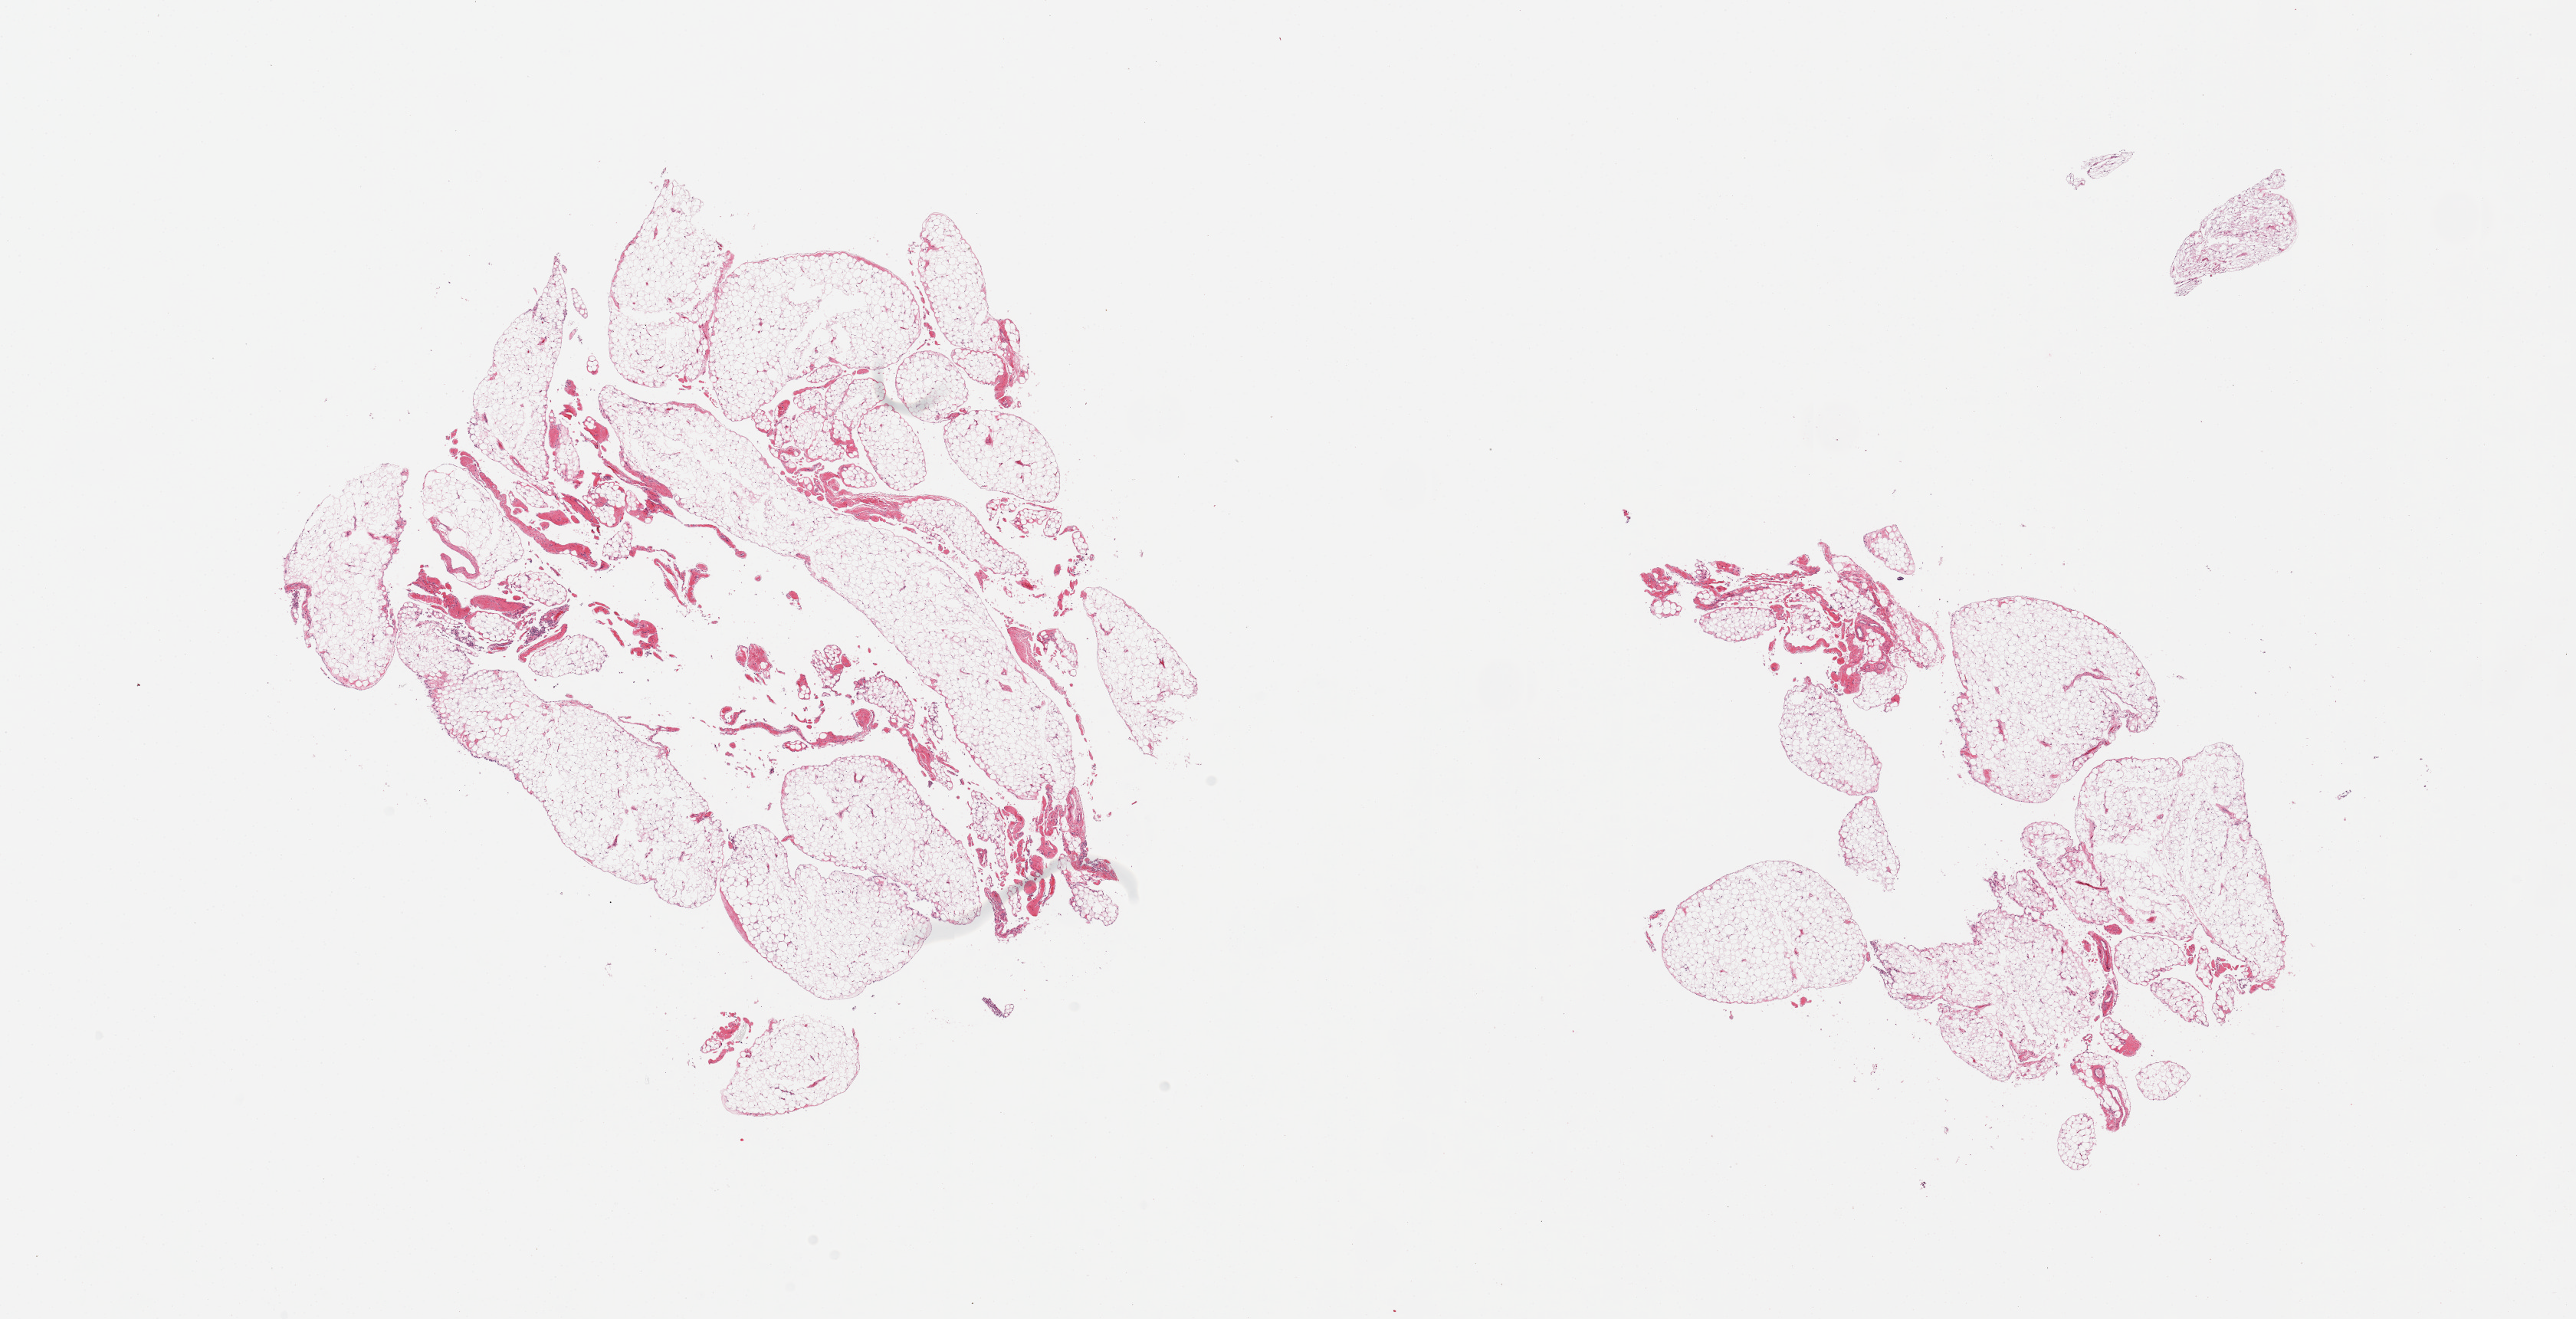
Haematoxylin and eosin whole-slide image — low-resolution overview of the scanned area, about 26.6 x 13.6 mm (acquisition: 20x scan), PAXgene-fixed, paraffin-embedded tissue, target tissue: omentum, donor tissue sample. Donor: male.
Review note (as recorded): 2 pieces; fat with dispersed small amounts of fibrovascular tissue.